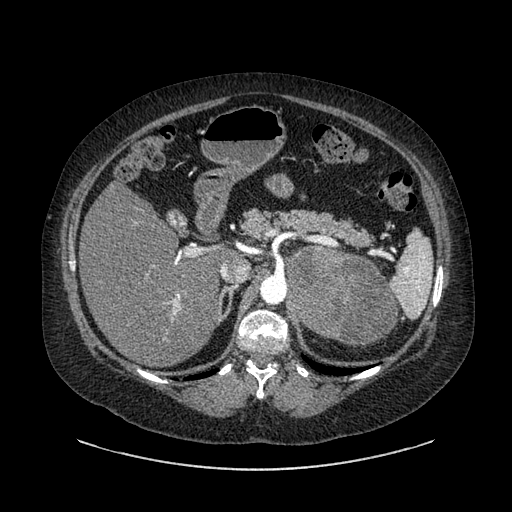
Contrast-enhanced abdominal CT, one axial slice; slice 583 of 769 in the series (ordered by position); 120 kVp; soft-tissue window (W 400 / L 40 HU); 0.62 mm slice thickness; 512 × 512 image matrix, field of view 460 × 460 mm. Patient: female, 61 years. From the clinical record (not read from this slice): diagnosis: adrenocortical carcinoma; tumour side: left adrenal; tumour size at pathology: 13 cm; Ki-67 index: 79 %.
Structures marked on this image (semi-automatic segmentation, software-assisted and operator-edited):
- mass: bounding box [x1, y1, x2, y2] px = [288, 248, 395, 345]